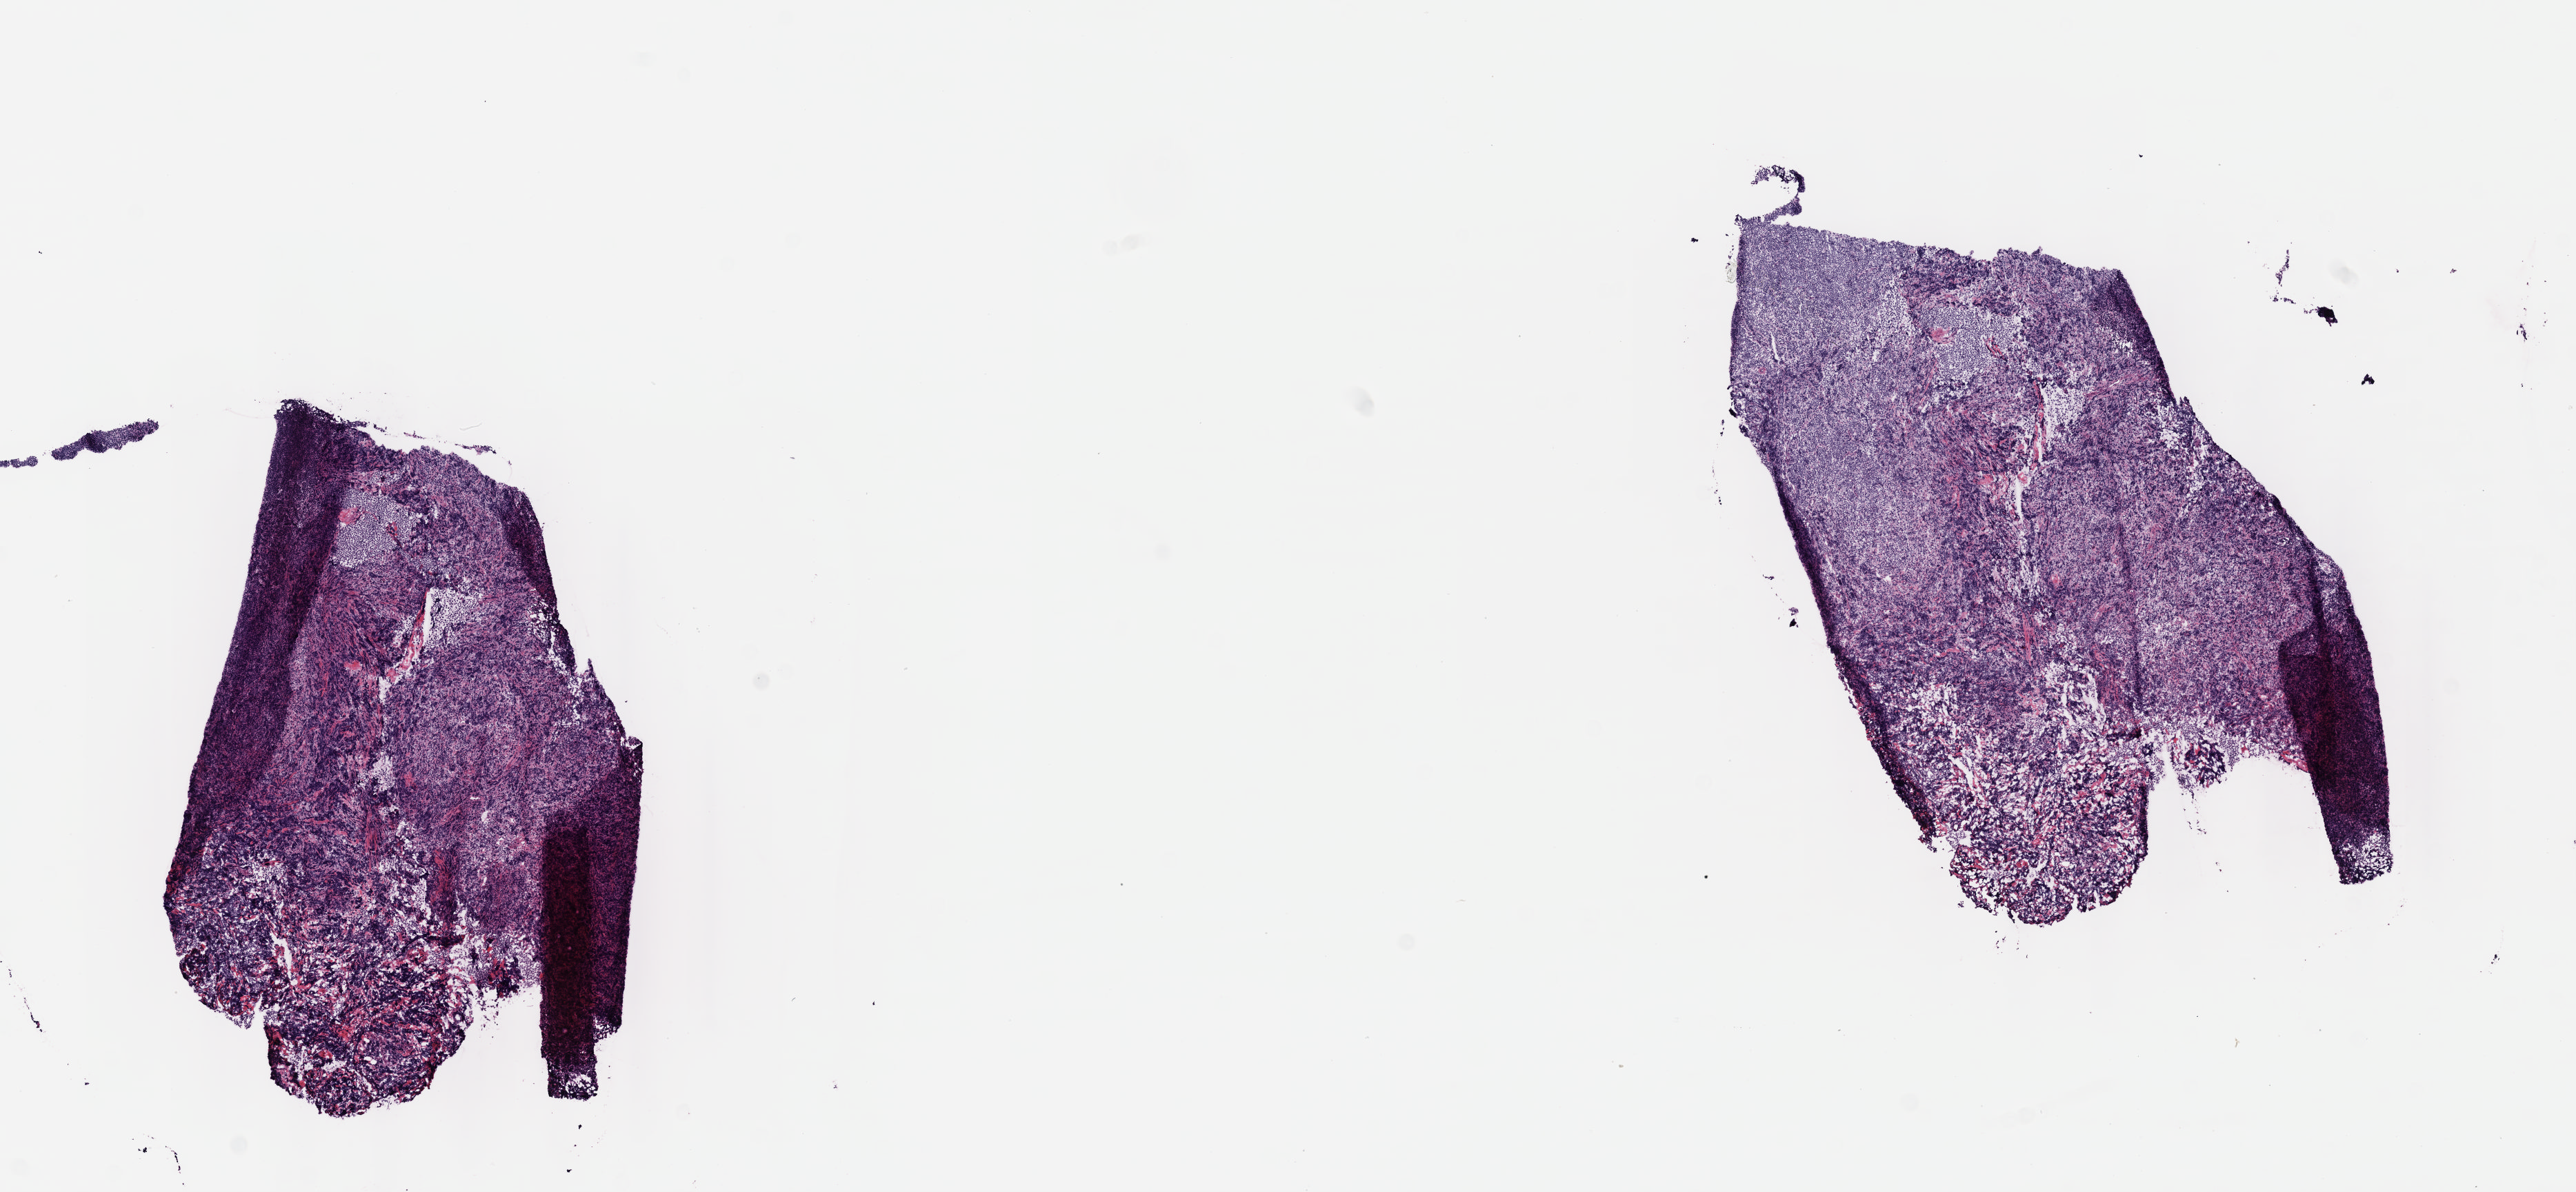
Whole-slide image, H&E stain, whole scanned area (about 15.1 x 7.0 mm) shown as a low-resolution overview. Frozen section. Primary tumor. Anatomic site: cranium. Female, age 8 years at initial diagnosis. Slide review estimates, as recorded: tumor cells 80%, tumor nuclei 80%, stromal cells 10%, necrosis 10%, normal cells 0%. Inflammatory infiltration, as recorded: lymphocyte infiltration 10%, monocyte infiltration 20%, neutrophil infiltration 25%.
* Ann Arbor stage (patient): Stage IV
* diagnosis: Burkitt lymphoma, NOS